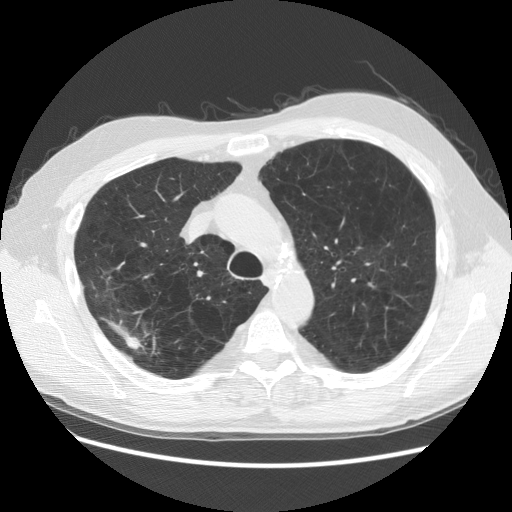
Low-dose screening chest CT, one axial slice; reconstruction kernel STANDARD; 140 kVp; lung window (W 1500 / L -600 HU); 2.5 mm slice thickness; 512 × 512 image matrix.
Annotated regions visible in this slice (outlined manually by an expert reader):
- lesion 2 (nodule, upper lobe of right lung): bounding box [x1, y1, x2, y2] px = [101, 317, 144, 350]